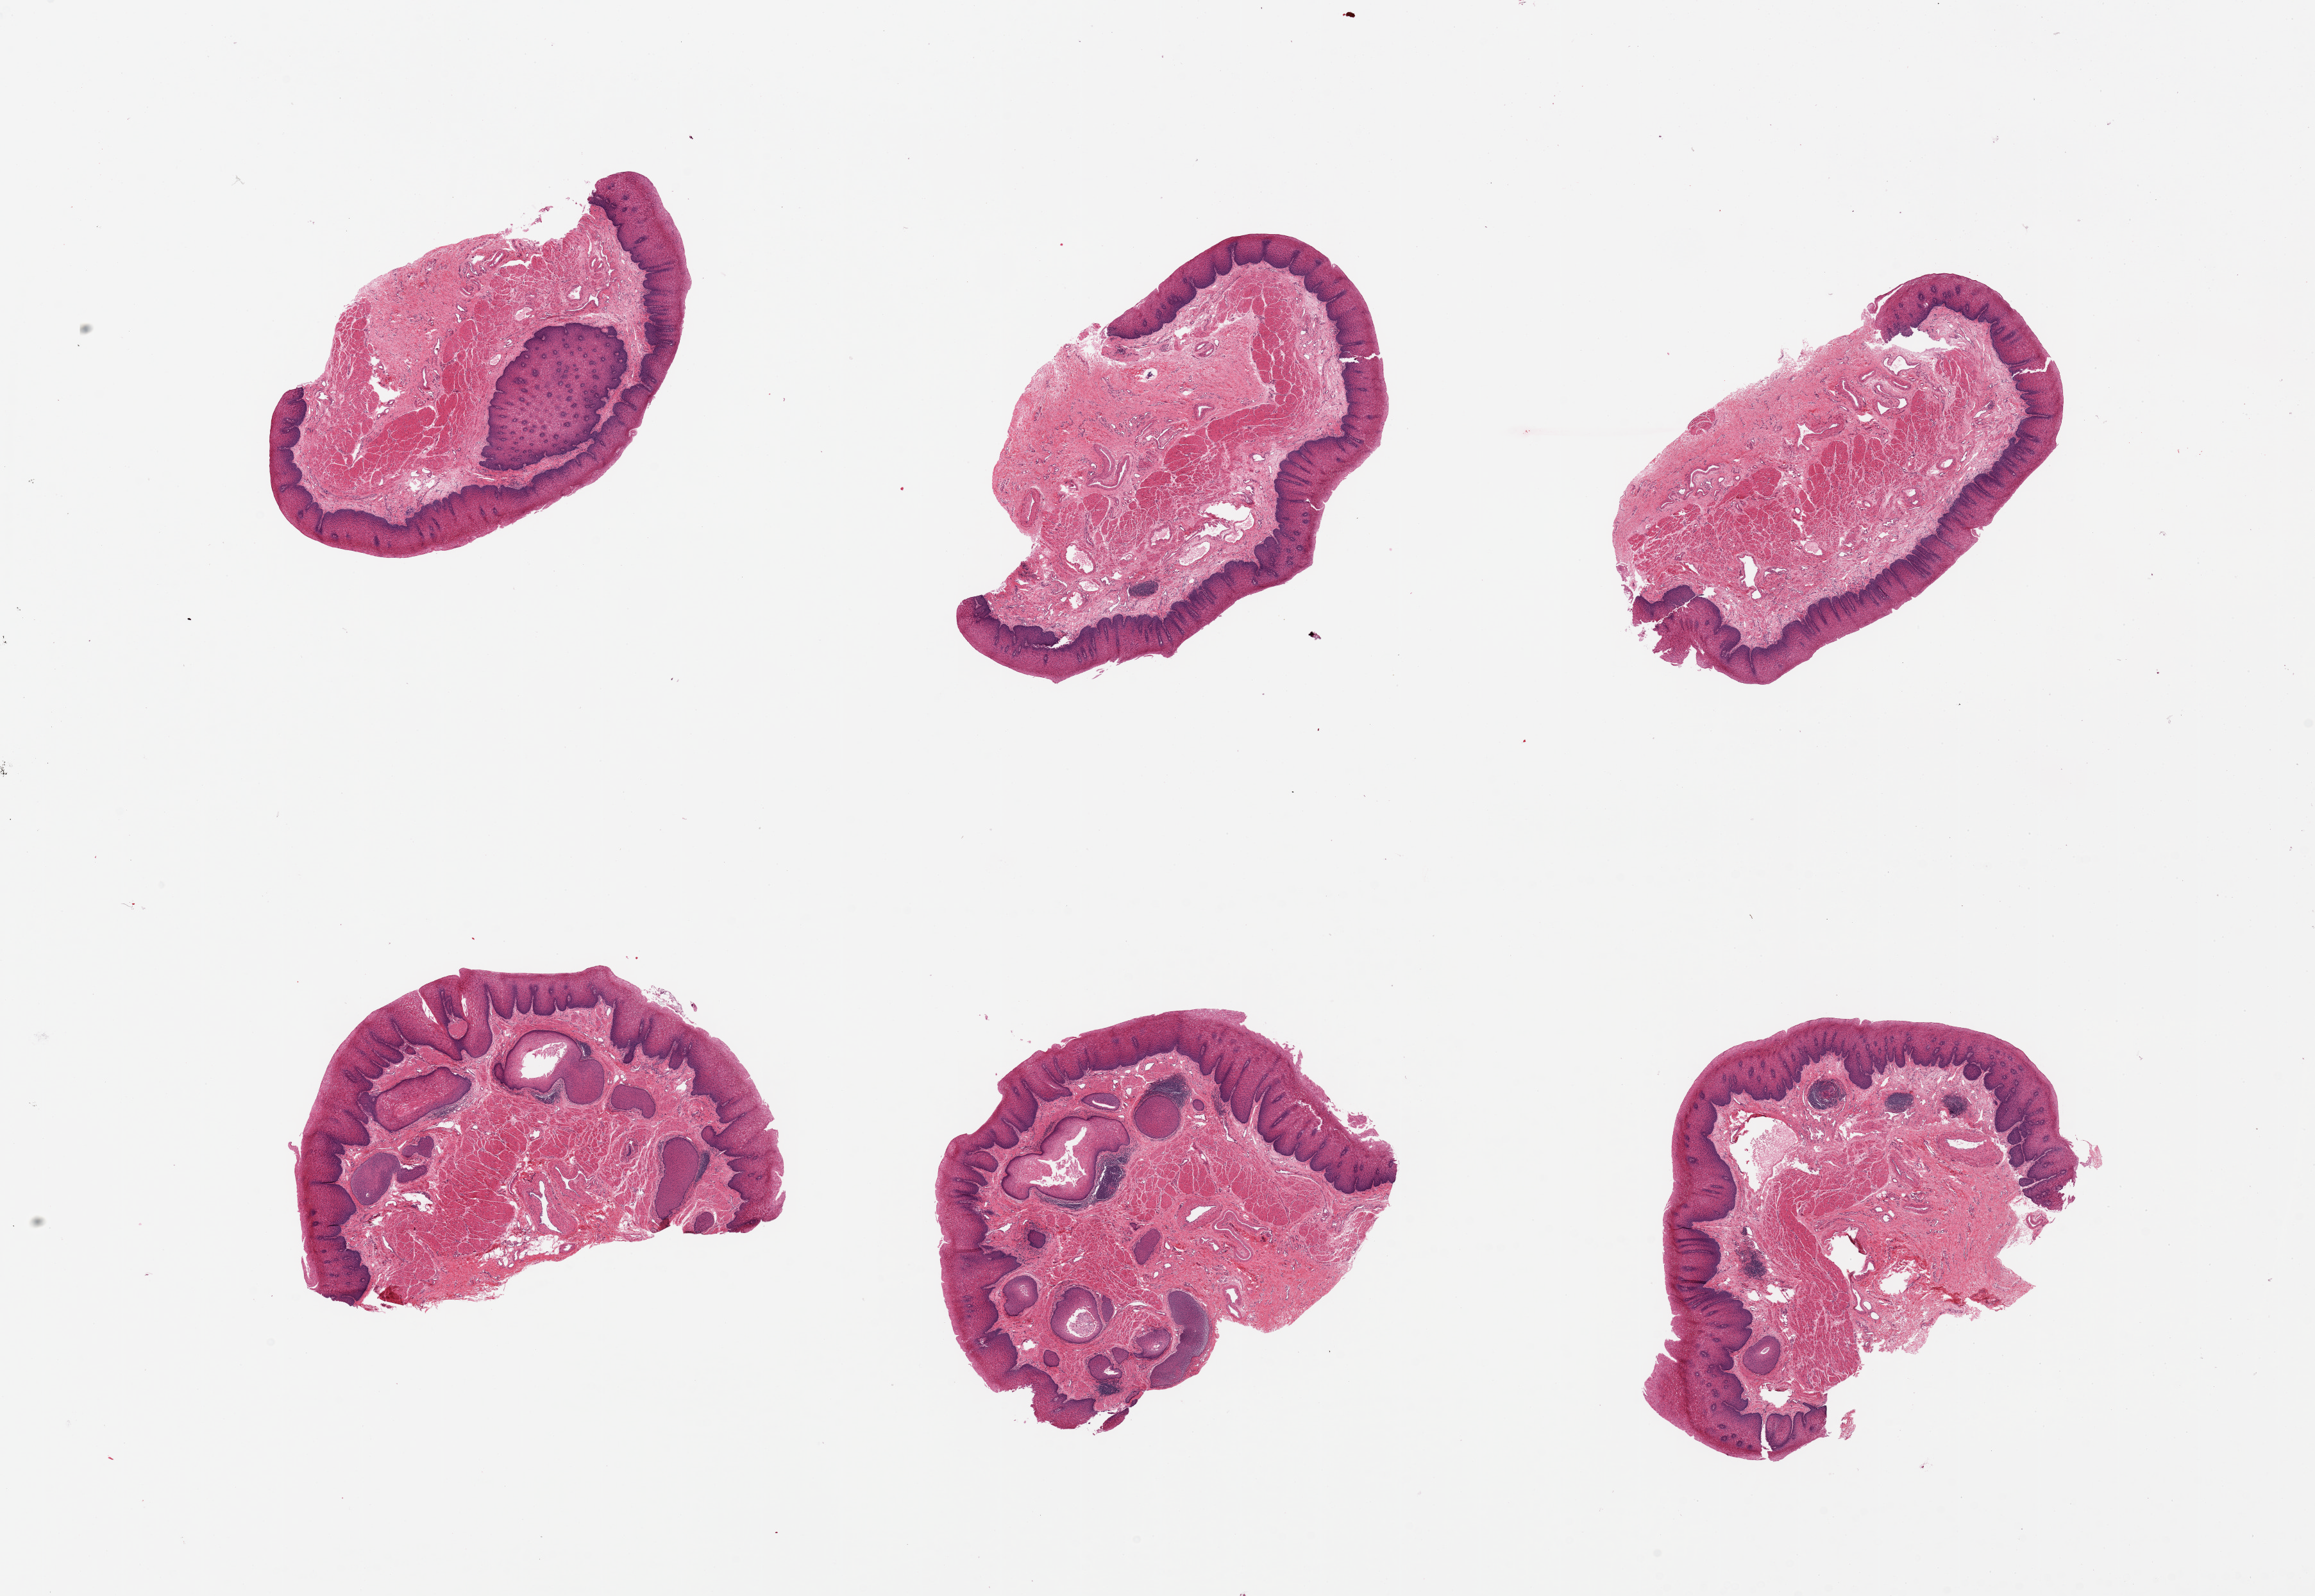
H&E whole-slide image, brightfield — whole scanned area (about 28.5 x 19.7 mm) shown as a low-resolution overview; PAXgene-fixed, paraffin-embedded tissue; target tissue: esophageal mucous membrane; tissue donor sample.
Pathologist's review note for this sample: 6 pieces. Moderate squamous hyperplasia (0.5 mm).